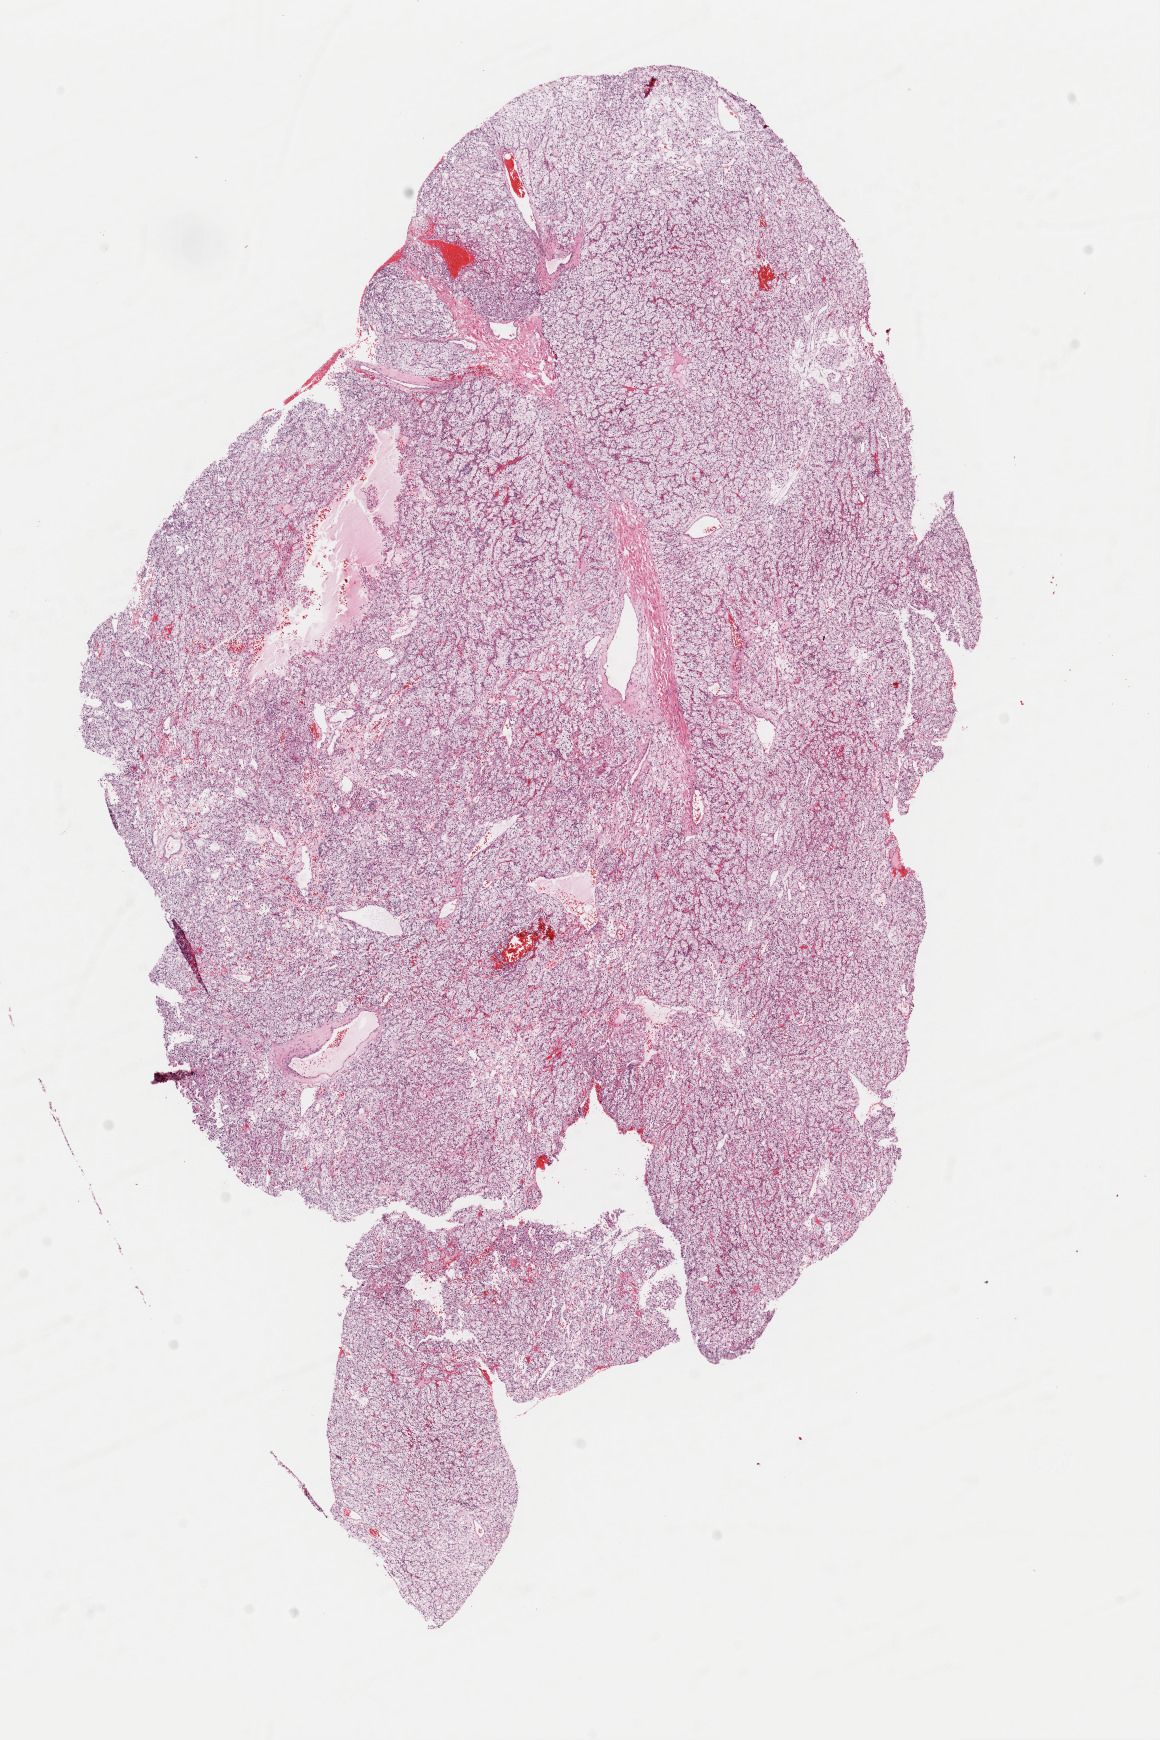
Digitized Hematoxylin and eosin (H&E) stained tissue section (whole slide) — low-resolution overview of the scanned area, about 9.2 x 13.7 mm. Frozen section from the top of the tissue portion. Sample: primary tumour, kidney. Male patient; age at initial diagnosis 73 years. Histologic grade: G2 (moderately differentiated). Pathologist review of this section (percent, as recorded): tumour cells 80%, tumour nuclei 92%, normal cells 0%, stromal cells 20%, necrosis 0%. Inflammatory infiltration, as recorded: lymphocyte infiltration 2%, monocyte infiltration 0%, neutrophil infiltration 0%.
• AJCC pathologic stage: I
• diagnosis: Clear cell adenocarcinoma, NOS